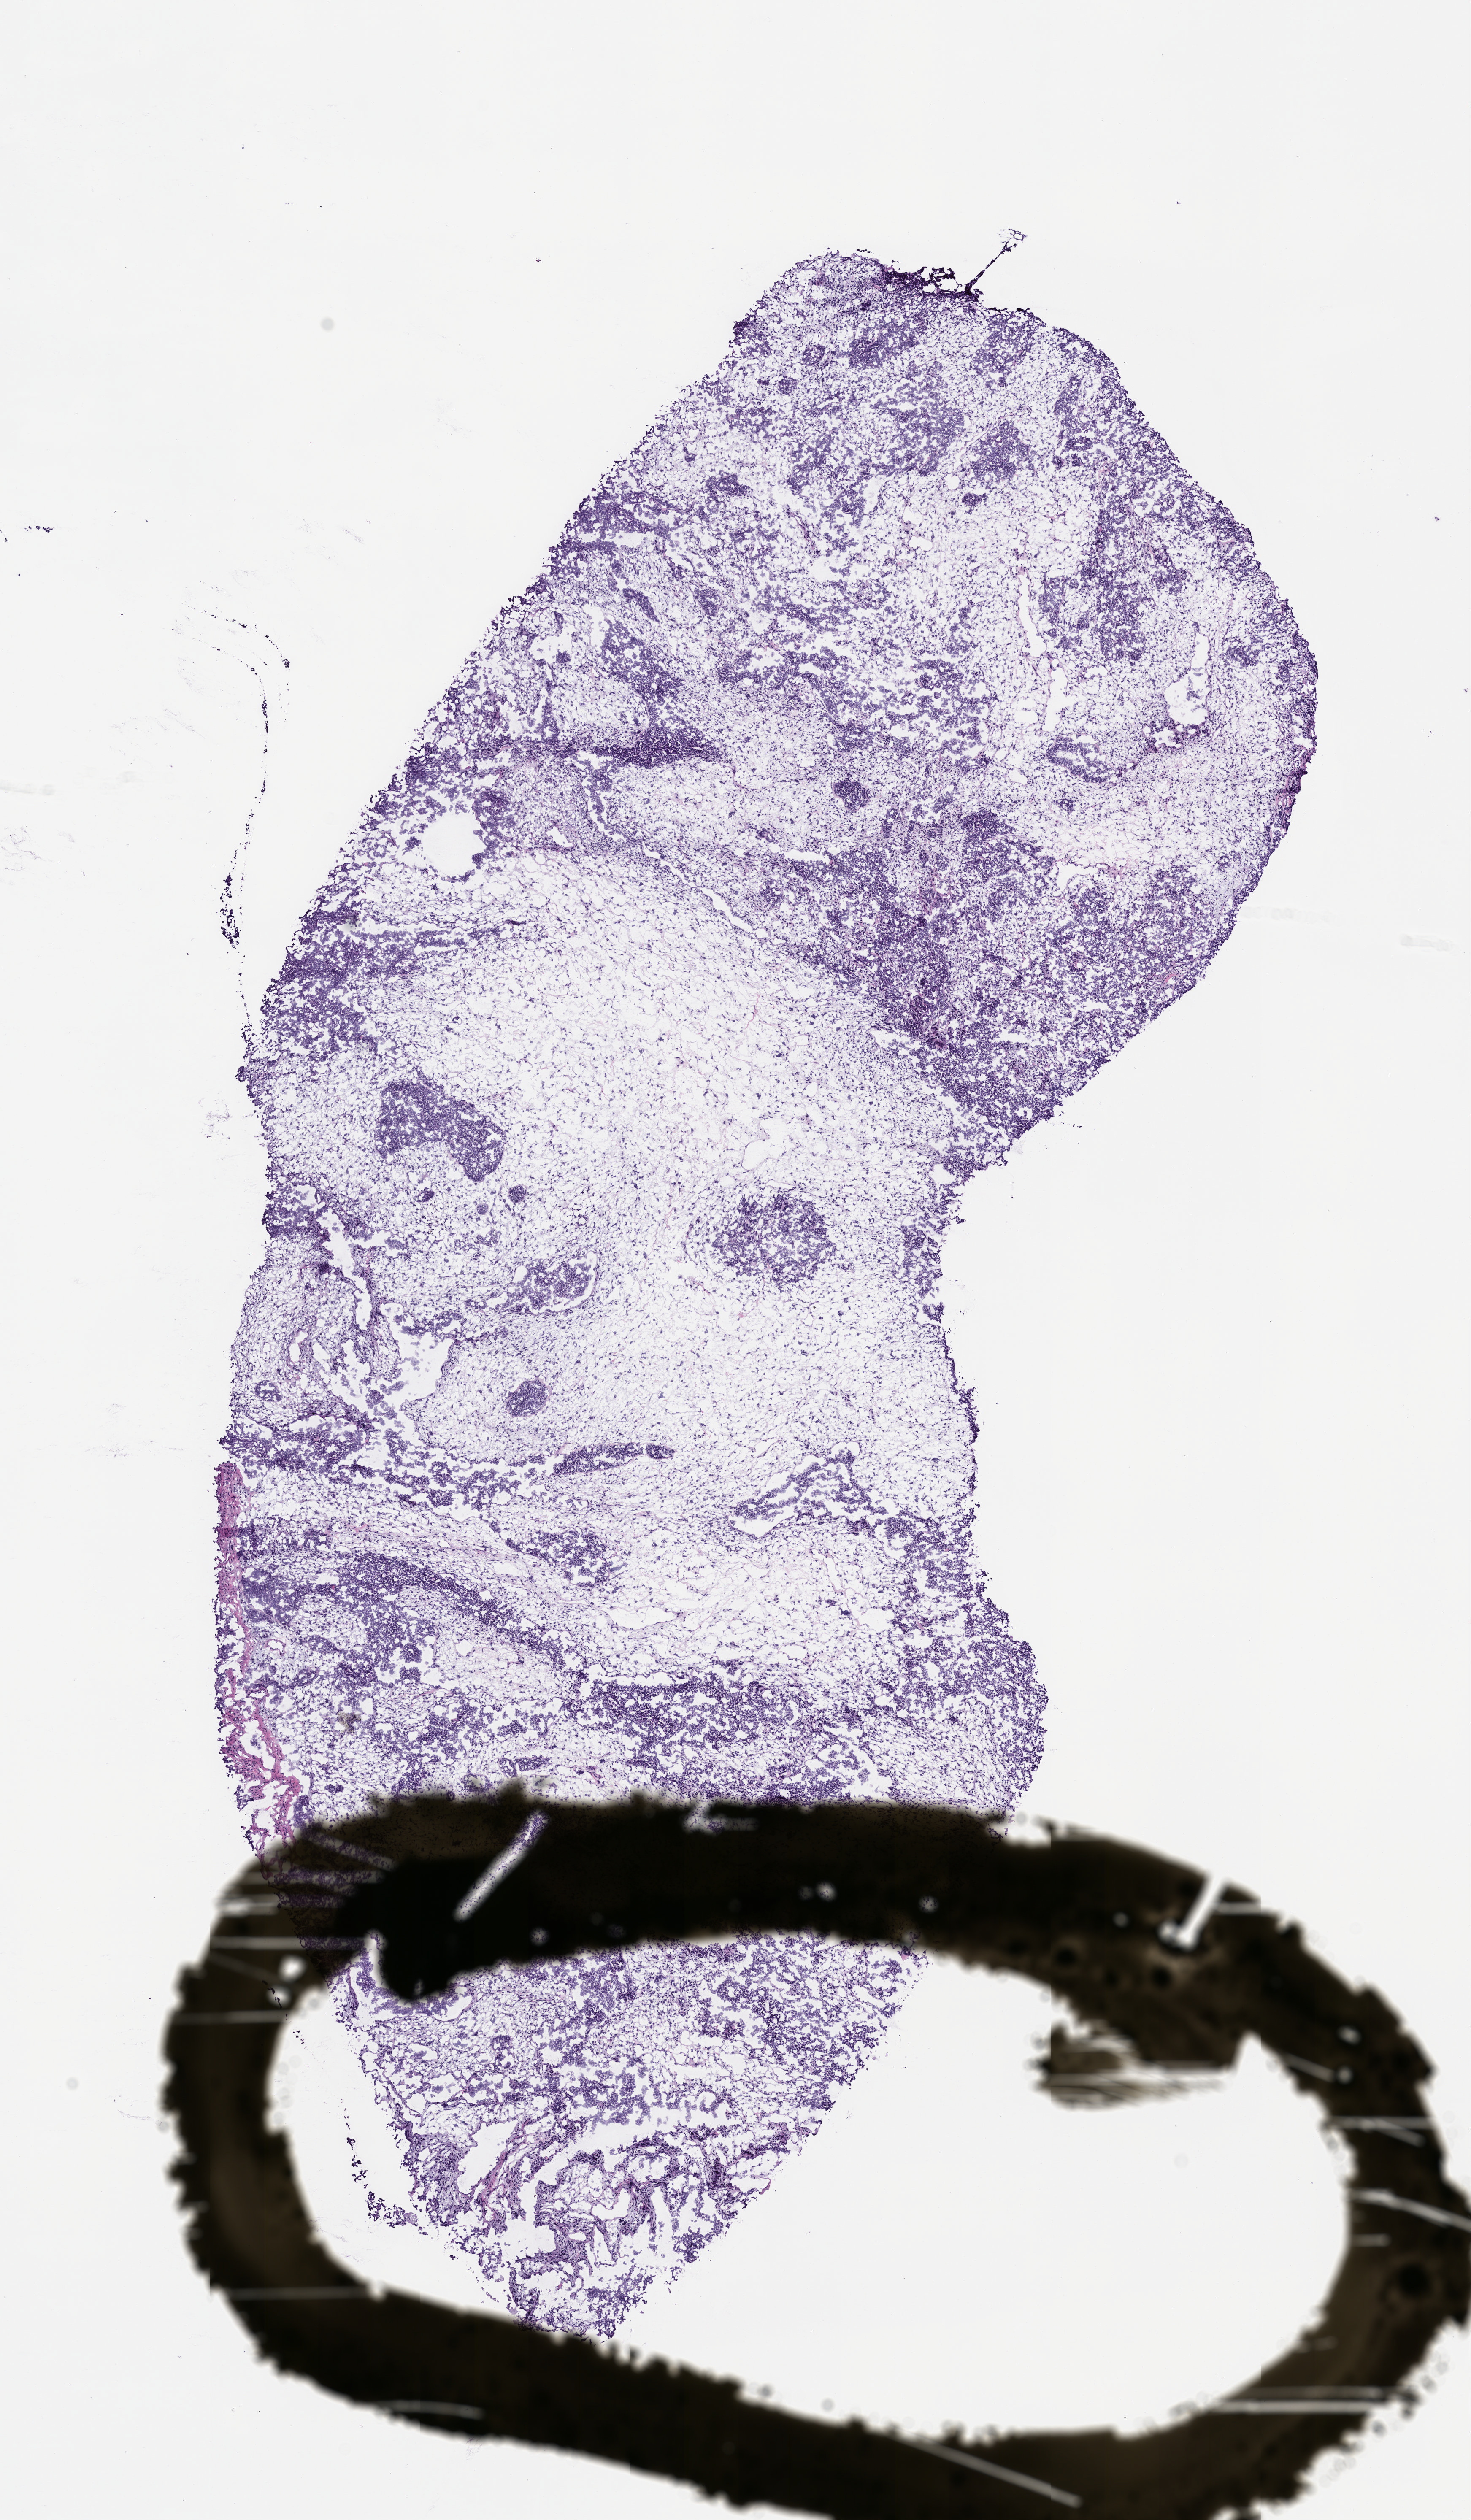
Hematoxylin and eosin (H&E) whole-slide image of a patient-derived xenograft (PDX) tumor grown in a mouse, shown as a low-resolution overview of the whole scanned area (about 7.0 x 12.0 mm). FFPE section. Originating tumor site category: uterus.
- originating patient diagnosis: Carcinosarcoma